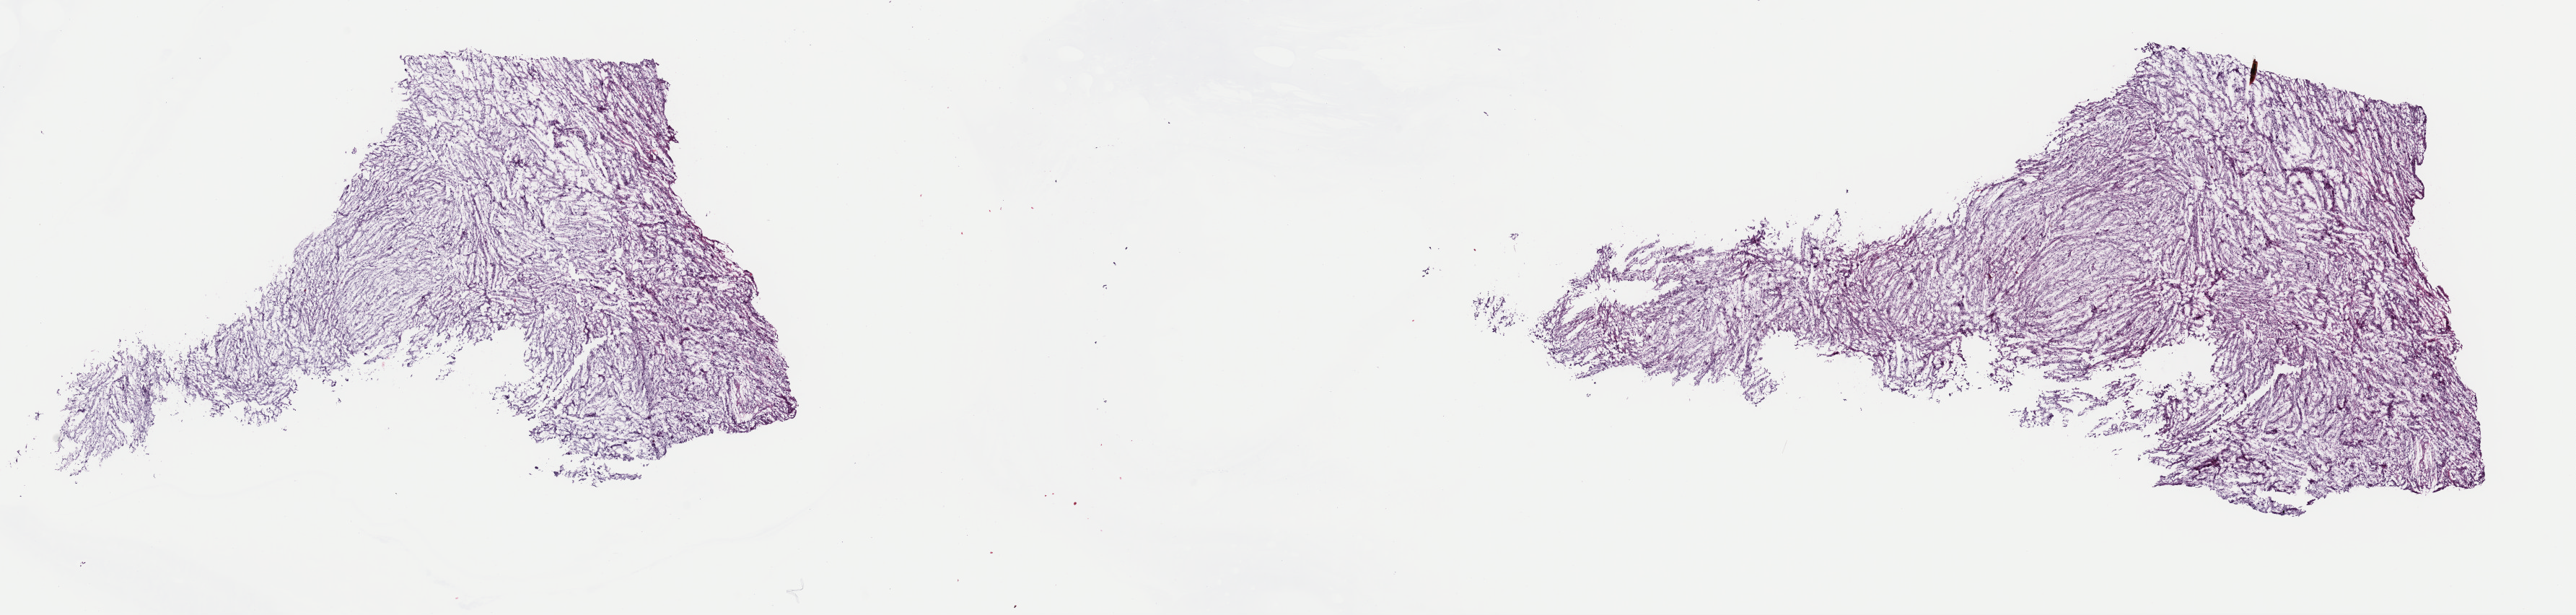
H&E-stained whole-slide image, low-resolution overview of the scanned area, about 28.2 x 6.7 mm (from a 40x scan). Frozen section from the top of the tissue portion. Connective, subcutaneous and other soft tissues, primary tumour sample. Male, age 61 years at initial diagnosis. Pathologist review of this section (percent, as recorded): tumour cells 100%, tumour nuclei 100%, normal cells 0%, stromal cells 0%, necrosis 0%. Infiltration values recorded for this section: lymphocyte infiltration 0%, monocyte infiltration 0%, neutrophil infiltration 0%.
* diagnosis: Fibromyxosarcoma (connective, subcutaneous and other soft tissues of pelvis)